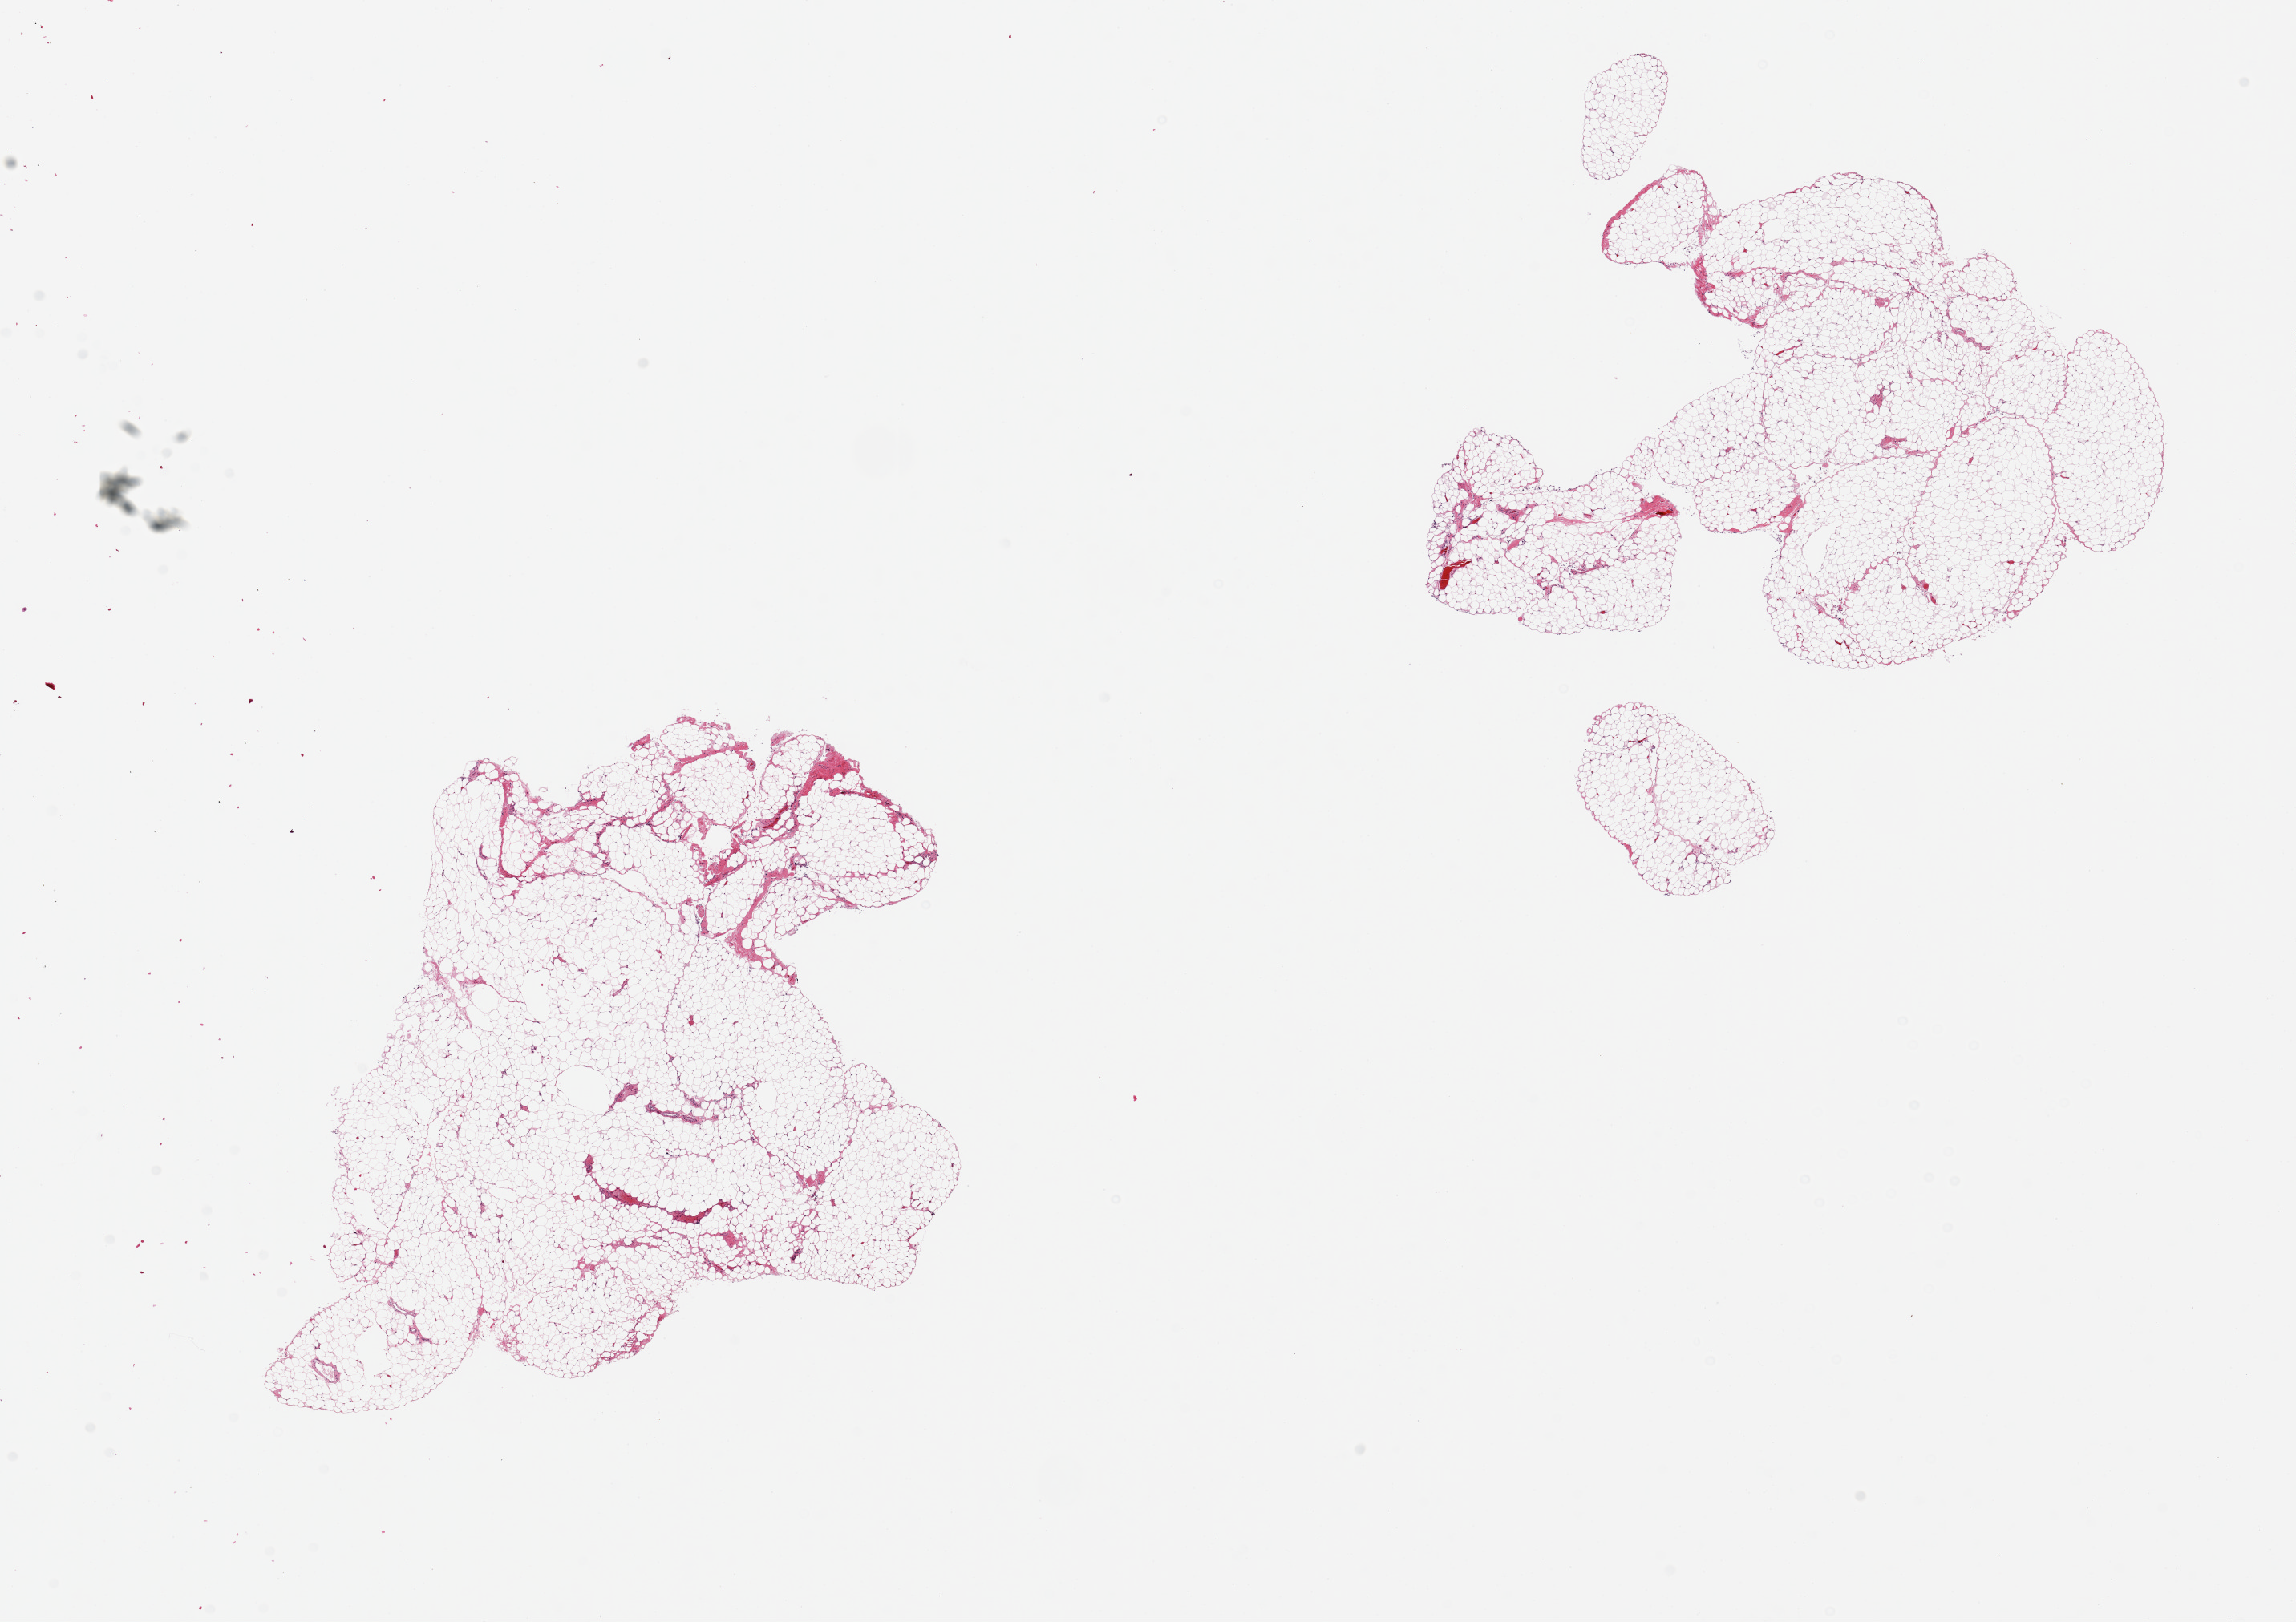
Whole-slide image, haematoxylin and eosin stain, a low-resolution overview of the entire scanned area, about 22.6 x 16.0 mm. PAXgene-fixed, paraffin-embedded tissue. Section of omentum (target tissue). Donor tissue sample.
• pathologist's review note for this sample: 2 pieces, 7x6 & 7x7mm